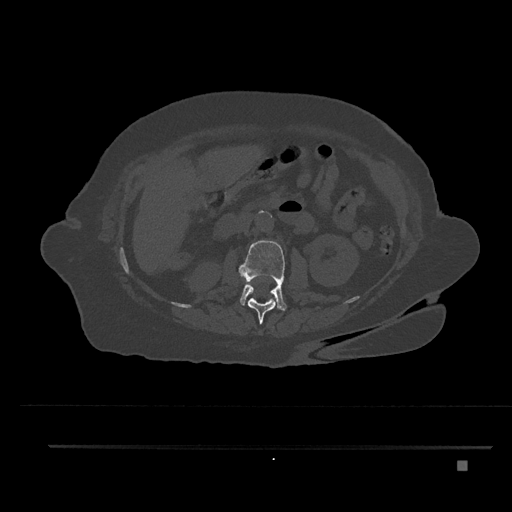
CT including the spine, one axial slice. Position 197 of 797 along the scan axis. Reconstruction kernel Br40s/3. 120 kVp. Bone window (W 1800 / L 400 HU). 512 × 512 image matrix, field of view 437 × 437 mm. Patient: female, 76 years. Case-level facts recorded for this patient, not image findings: primary cancer: lung; vertebrae with lytic lesions (as recorded): T11, L3.
Annotated regions visible in this slice (semi-automatically segmented with operator editing):
- L1 vertebra: bounding box (x1, y1, x2, y2) in pixels: (248, 298, 278, 324)
- L2 vertebra: (238, 240, 287, 311)